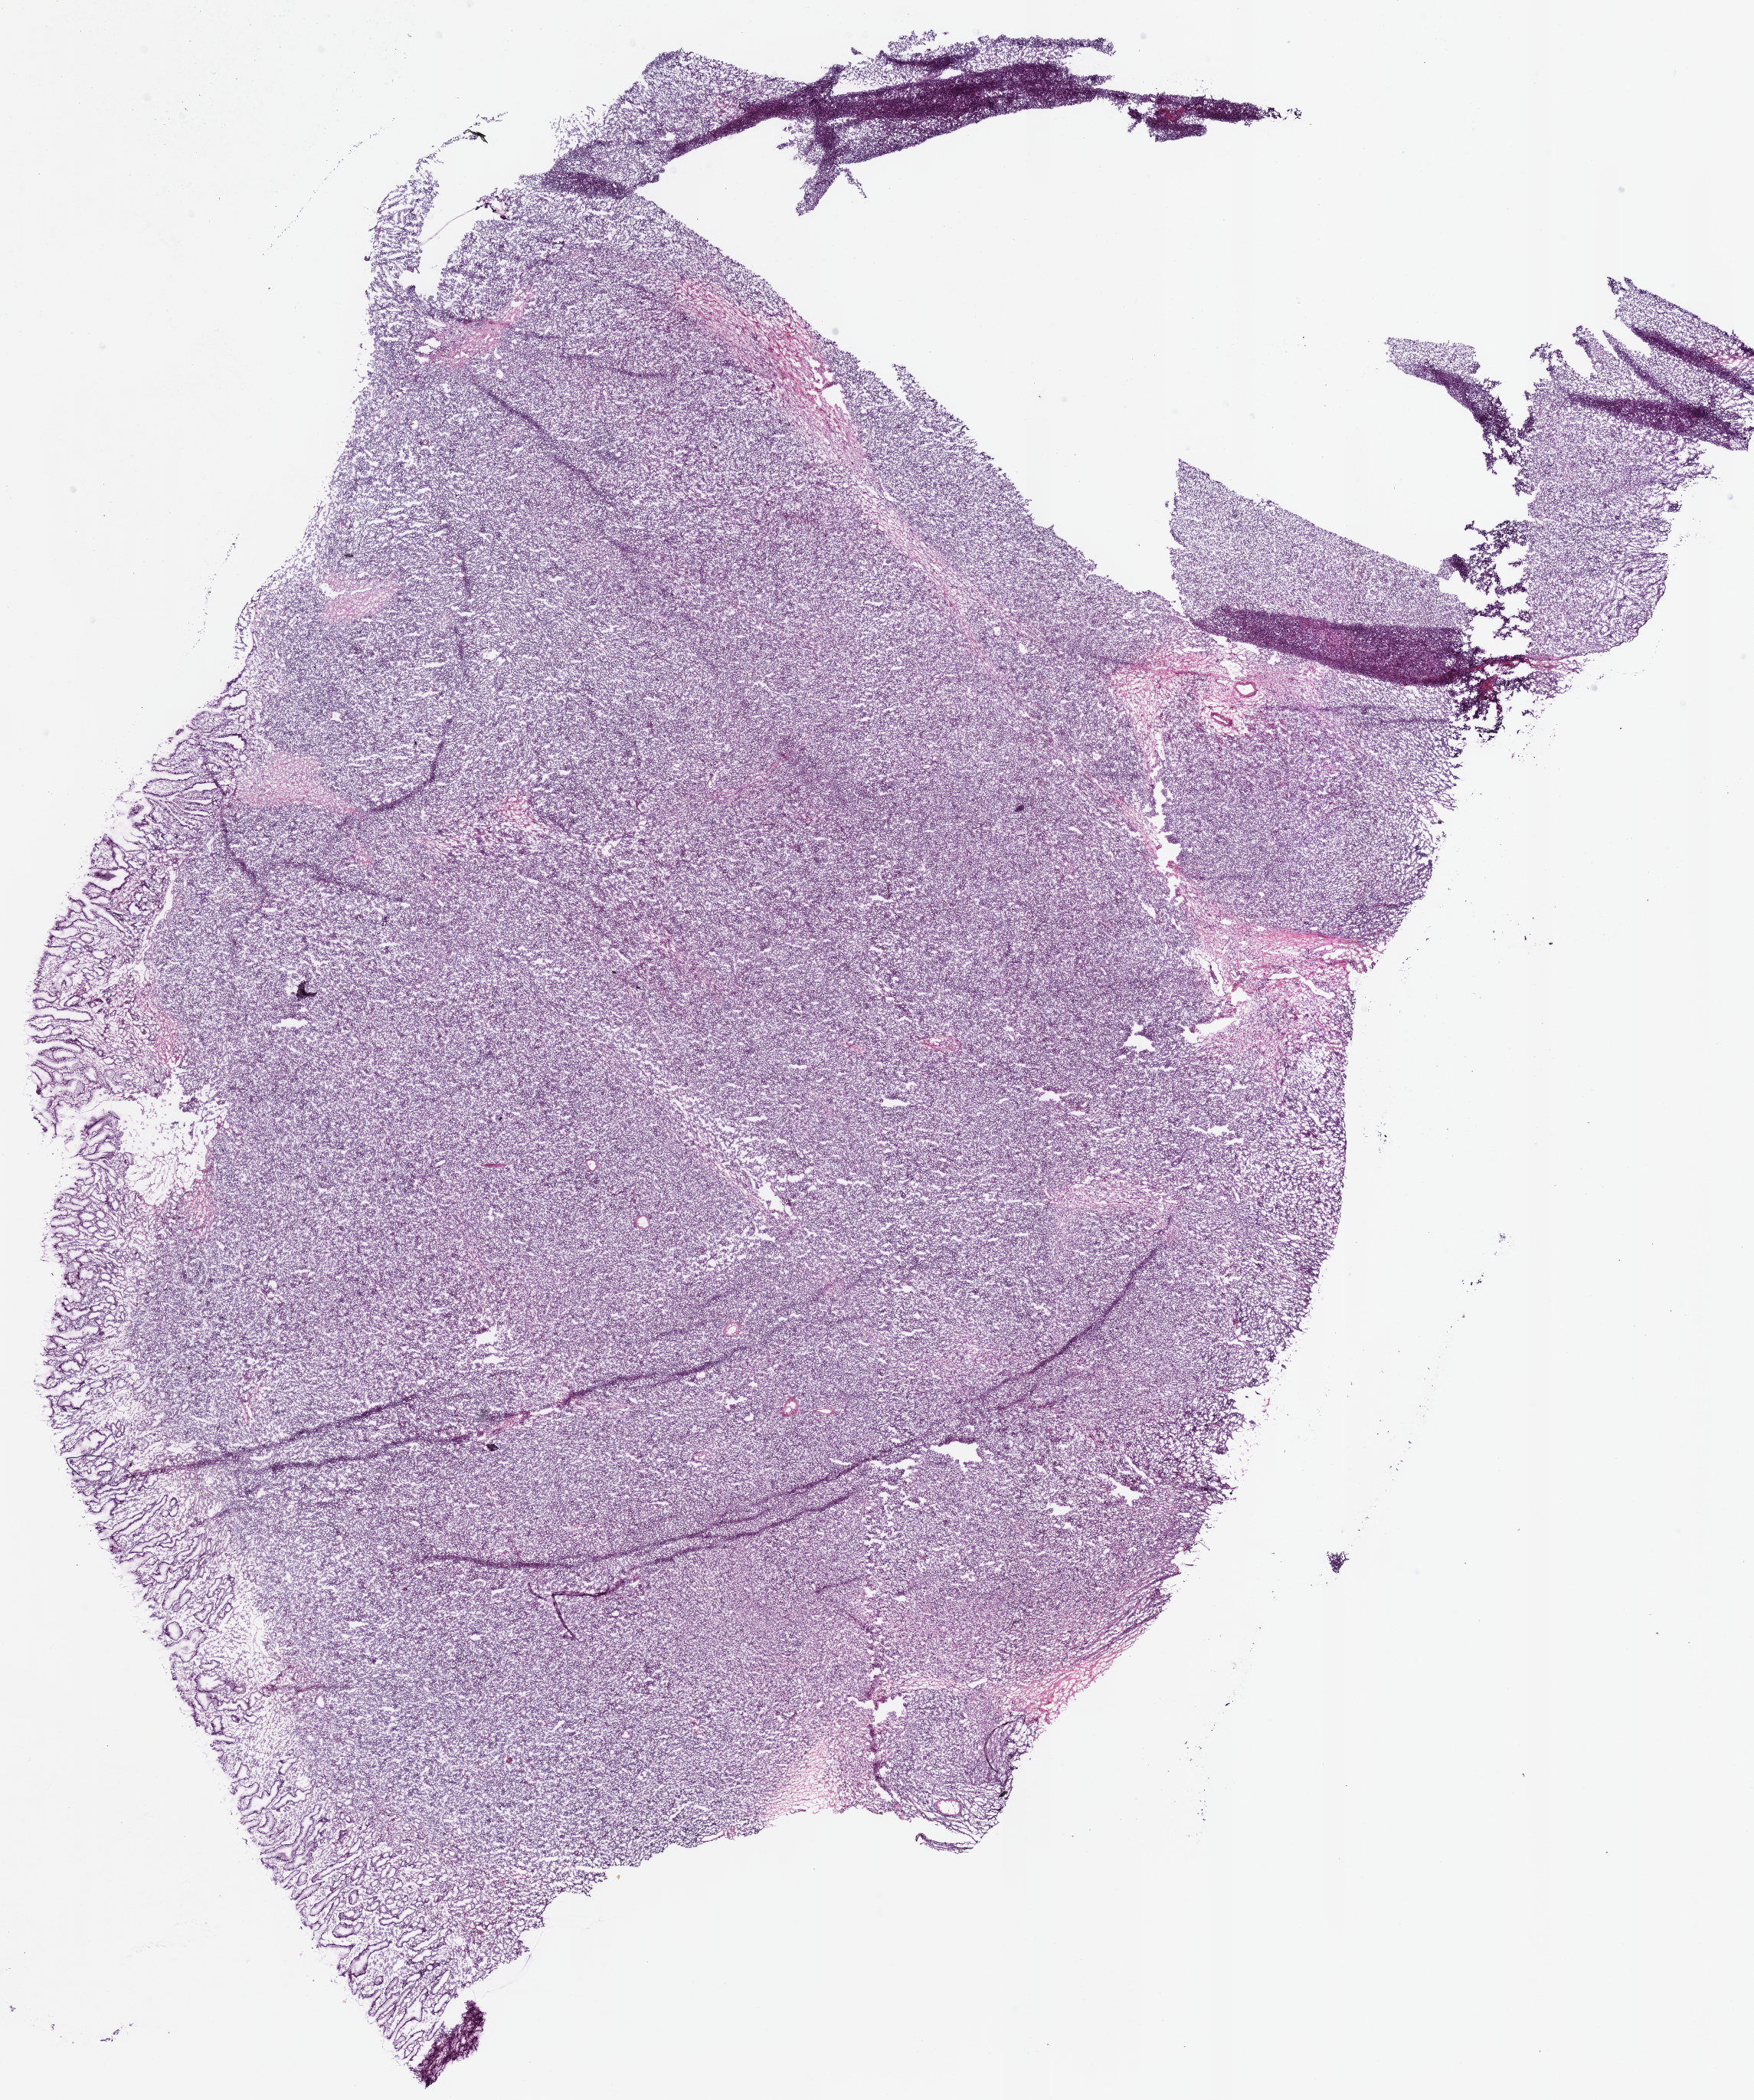
Digitized H&E tissue section (whole slide), whole scanned area (about 18.0 x 21.6 mm, slide scanned at 40x) shown as a low-resolution overview, frozen section from the bottom of the tissue portion, primary tumour sample from the lymphoid tissue. Male, age 75 years at initial diagnosis. Pathologist review of this section (percent, as recorded): tumour cells 90%, tumour nuclei 80%, normal cells 10%, stromal cells 0%, necrosis 0%. Infiltration values recorded for this section: lymphocyte infiltration 90%, monocyte infiltration 0%, neutrophil infiltration 5%.
Diagnosis: Diffuse large B-cell lymphoma, NOS (stomach, NOS).